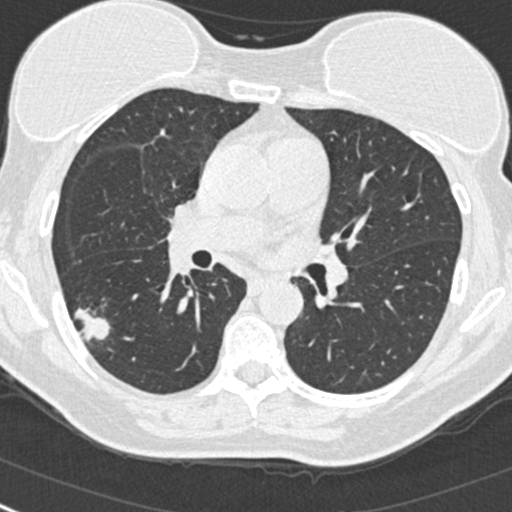
Low-dose screening chest CT, one axial slice; position 148 of 268 along the scan axis; lung window (W 1500 / L -600 HU); 1 mm slice thickness; 512 × 512 image matrix, field of view 296 × 296 mm.
Annotated regions visible in this slice (manually delineated by an expert):
- lesion 1 (tumor, upper lobe of right lung): bounding box (x1, y1, x2, y2) in pixels: (75, 308, 111, 341)